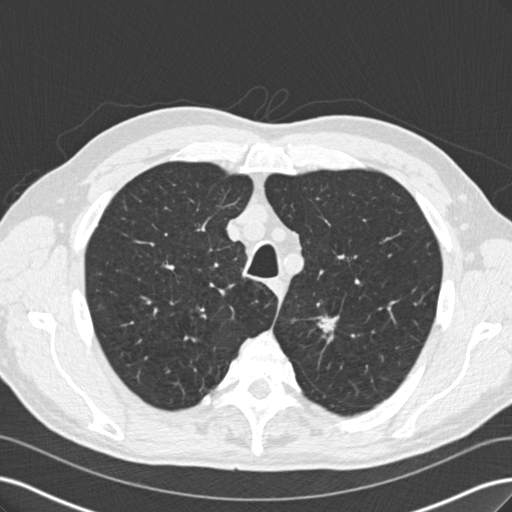
Low-dose screening chest CT, one axial slice. Slice 178 of 219 in the series (ordered by position). Reconstruction kernel B30f. 120 kVp. Lung window (W 1500 / L -600 HU). 2 mm slice thickness. 512 × 512 image matrix, field of view 360 × 360 mm.
Structures marked on this image (manually delineated by an expert):
- lesion 1 (tumor, upper lobe of left lung): bounding box (x1, y1, x2, y2) in pixels: (317, 314, 339, 333)